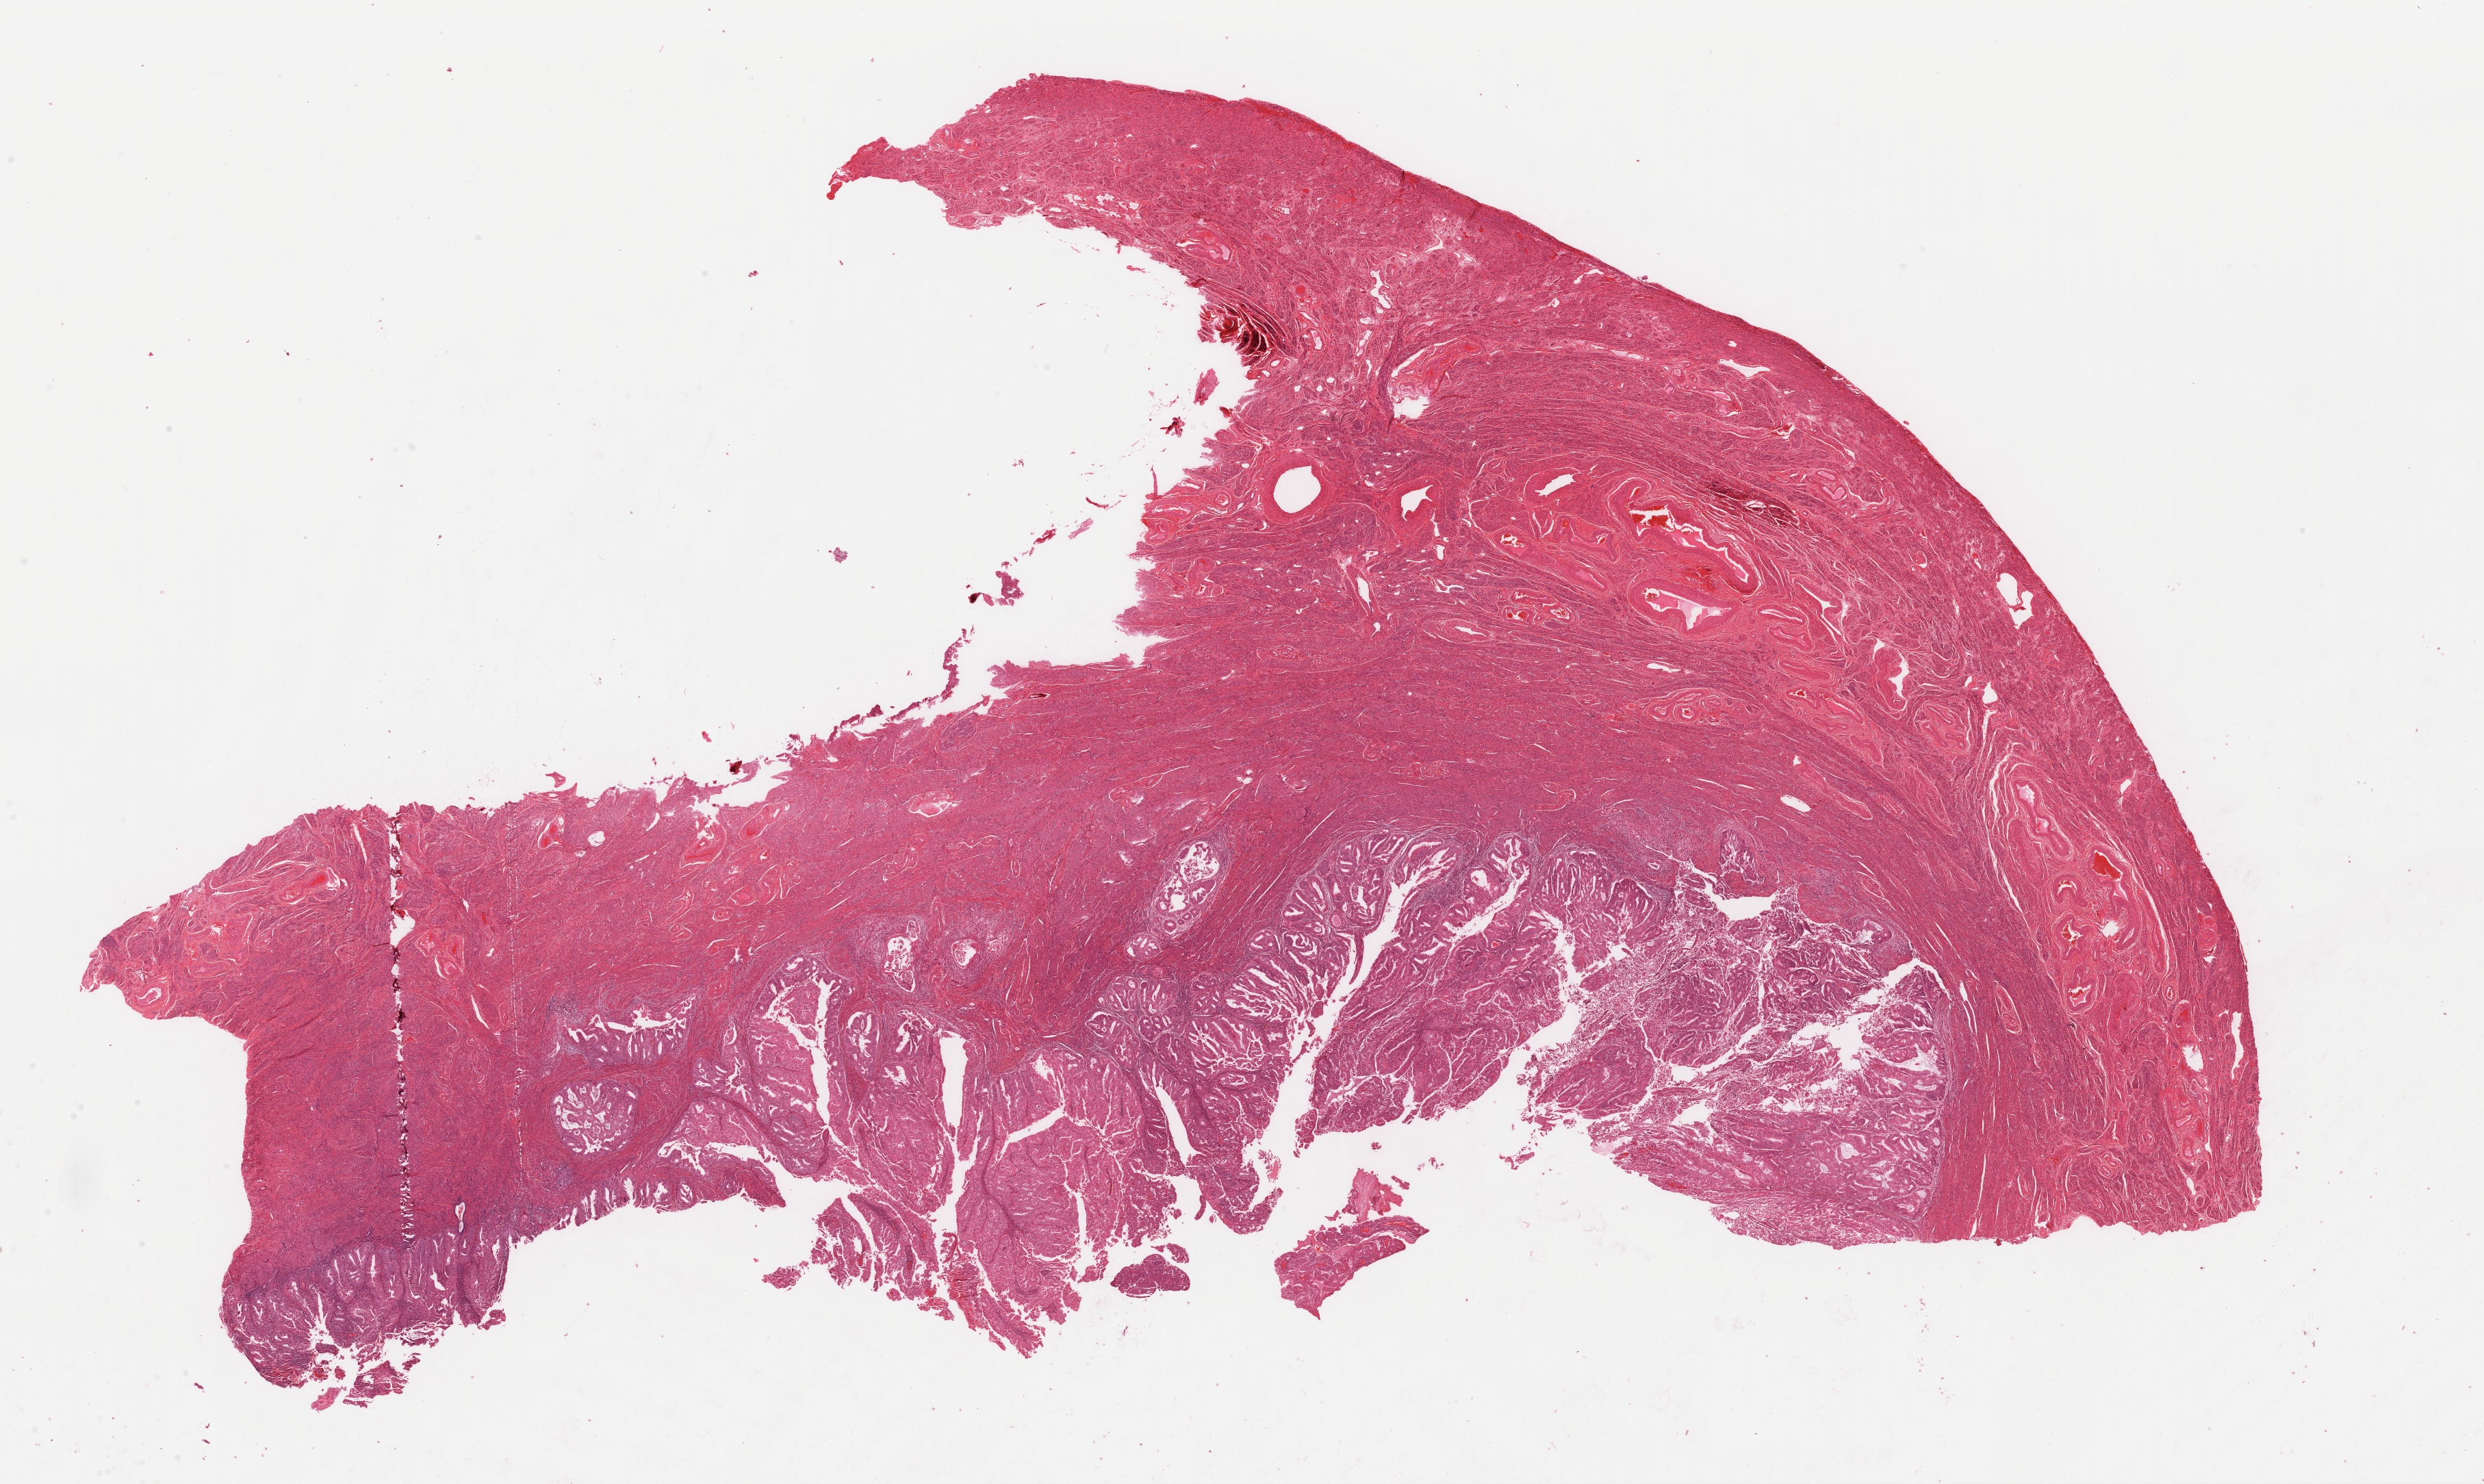
Whole-slide histology image, H&E, whole scanned area (about 28.7 x 17.1 mm, slide scanned at 40x) shown as a low-resolution overview; formalin-fixed paraffin-embedded (FFPE) diagnostic section; uterus, primary tumour sample. Patient: female, age at initial diagnosis 60 years. Histologic grade: G1 (well differentiated).
Diagnosis: Endometrioid adenocarcinoma, NOS (endometrium). FIGO stage: IIB.